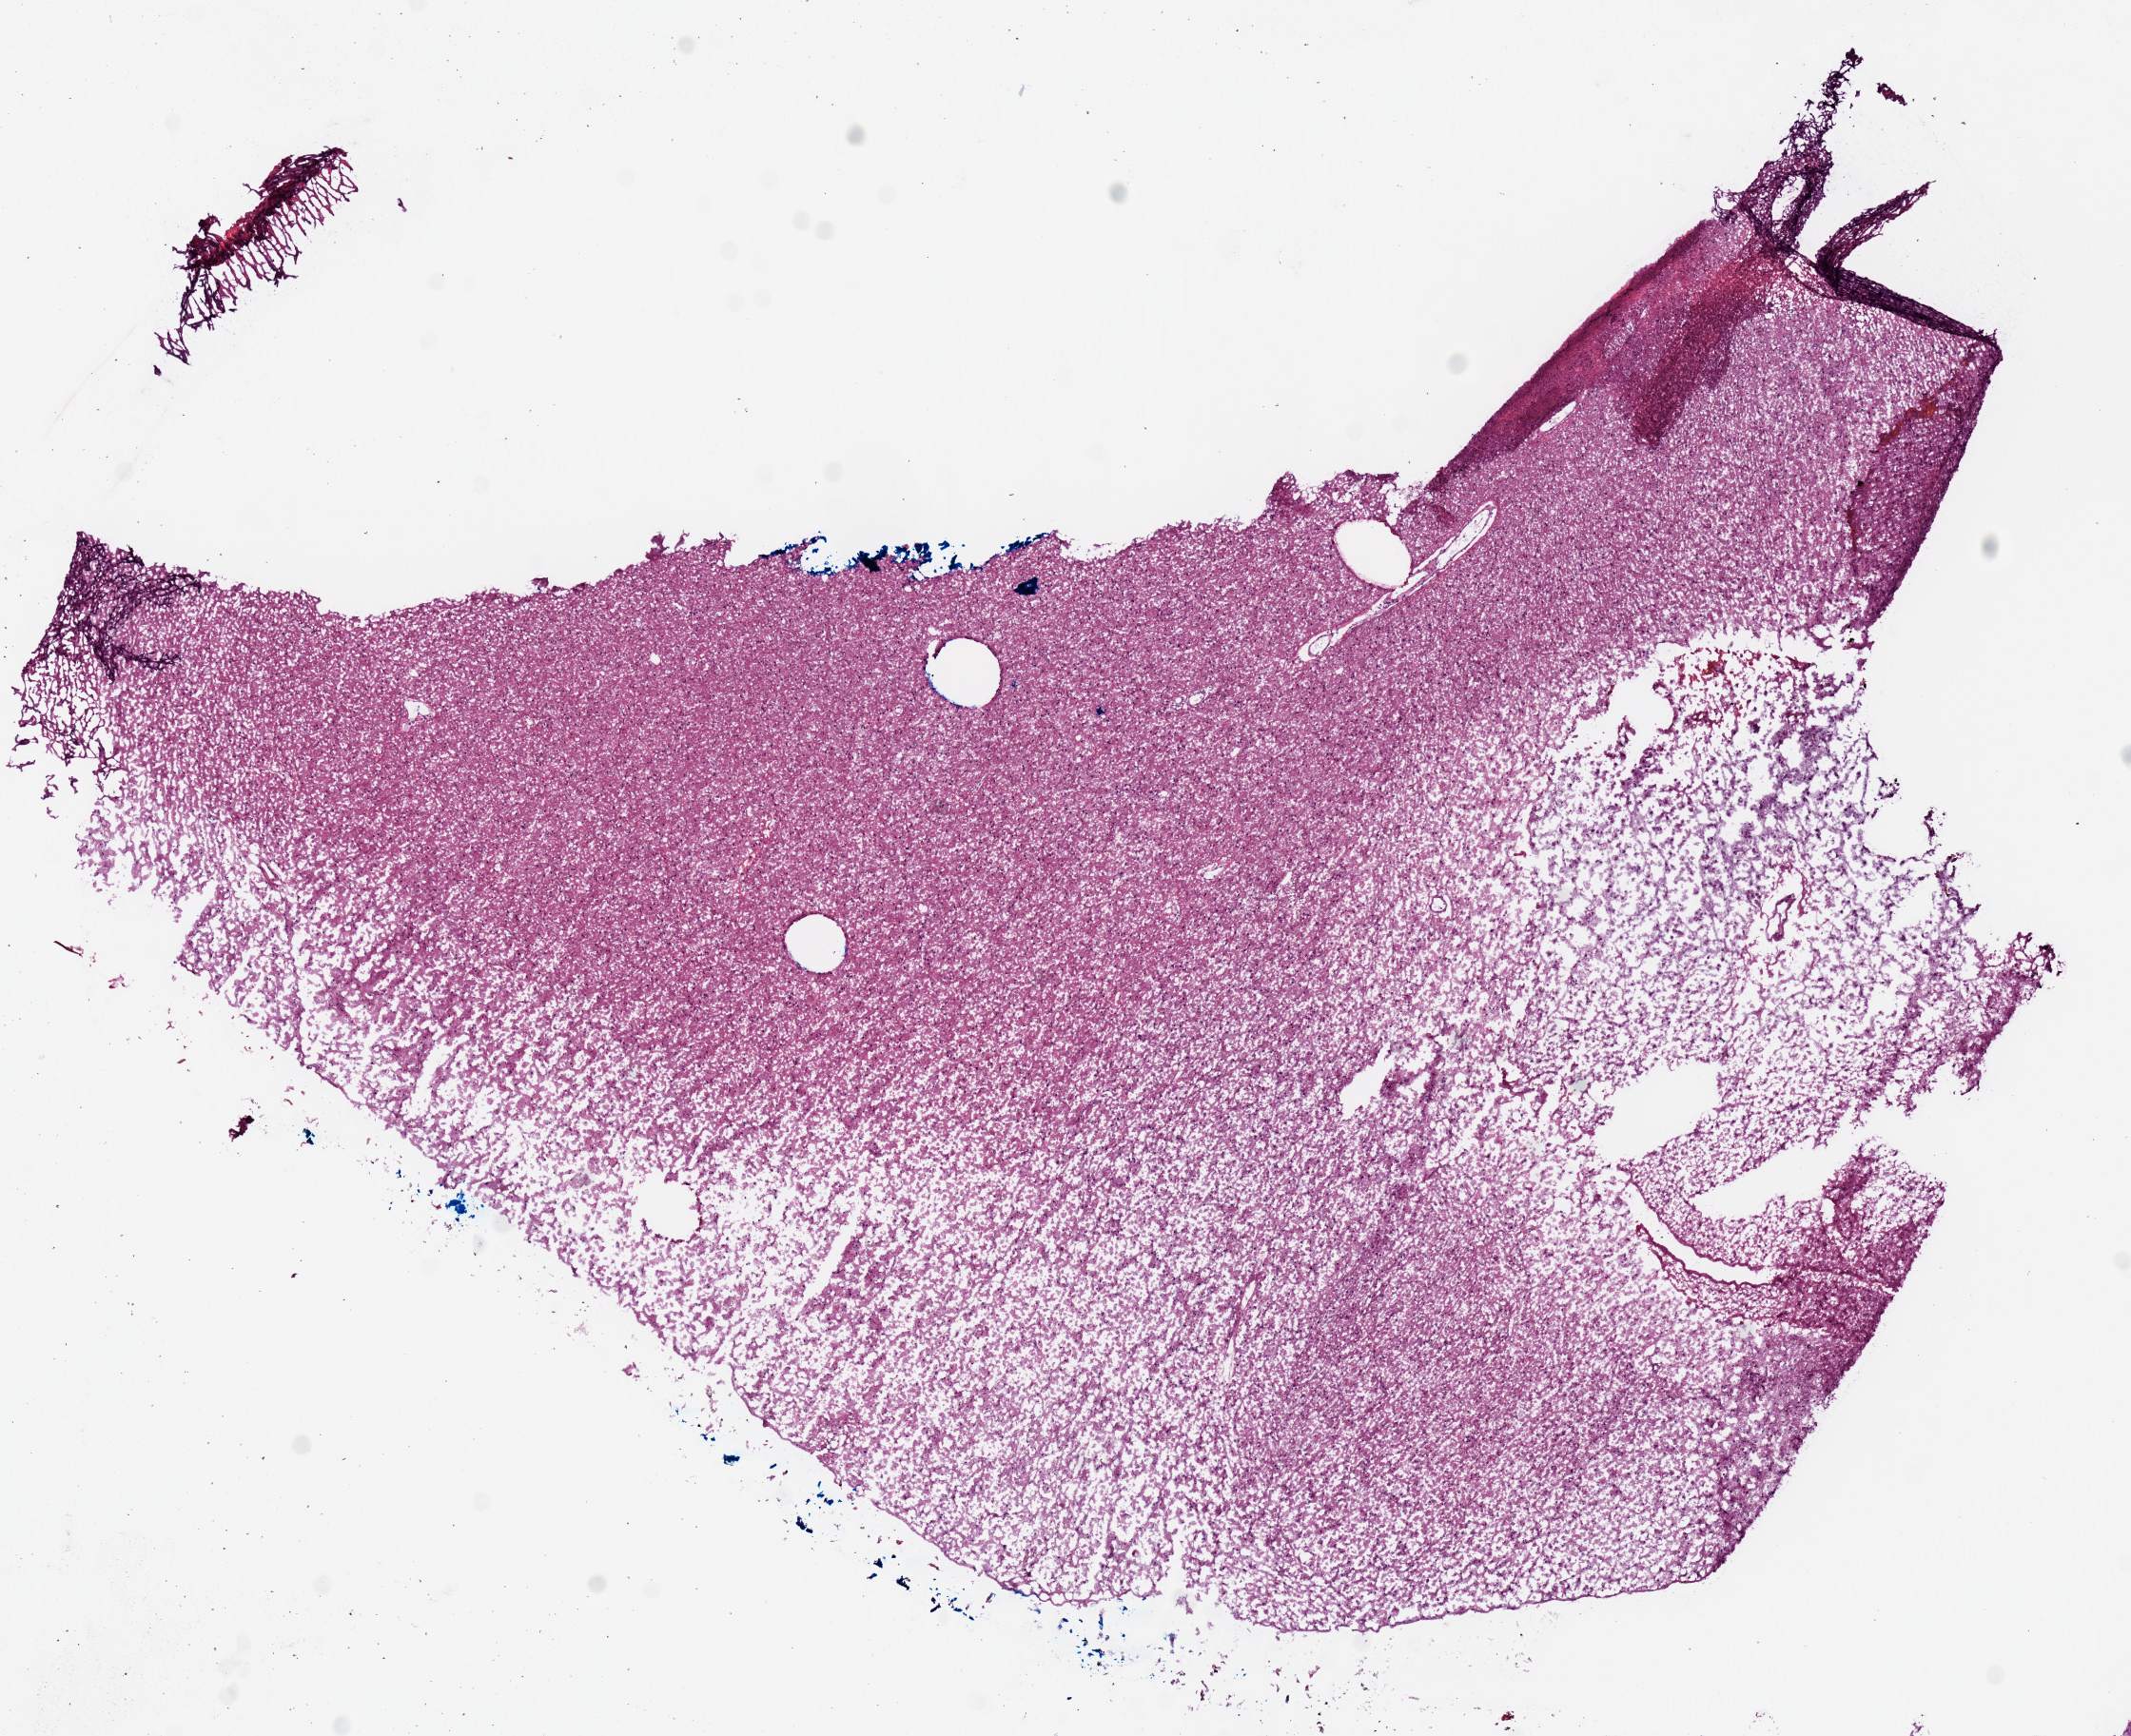
H&E whole-slide image, whole scanned area (about 8.9 x 7.2 mm, from a 20x scan) shown as a low-resolution overview, frozen section from the top of the tissue portion, brain, primary tumour sample. Male patient; age at initial diagnosis 30 years. Histologic grade: G3 (poorly differentiated). Slide review estimates, as recorded: tumour nuclei 65%, necrosis 0%.
Pathologic diagnosis: Oligodendroglioma, anaplastic (cerebrum).